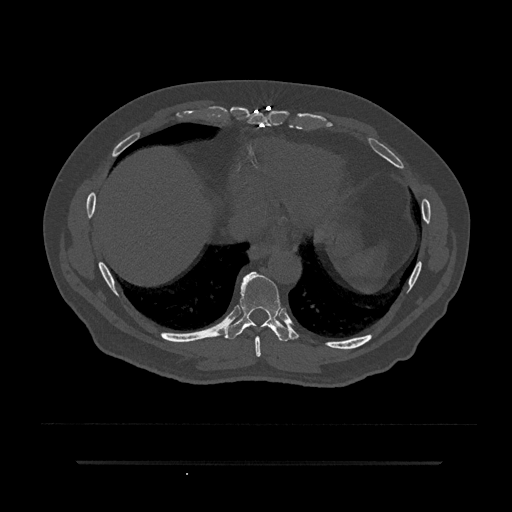
CT including the spine, one axial slice; slice 391 of 797 in the series (ordered by position); reconstruction kernel Br40s/3; 120 kVp; bone window (W 1800 / L 400 HU); 512 × 512 image matrix, field of view 464 × 464 mm. Male patient, age 59 years. From the clinical record (not read from this slice): primary cancer: bile ducts.
Structures marked on this image (semi-automatic segmentation, software-assisted and operator-edited):
- T8 vertebra: box from (x=255, y=336) to (x=261, y=357) px
- T9 vertebra: (x=227, y=271)–(x=291, y=342)